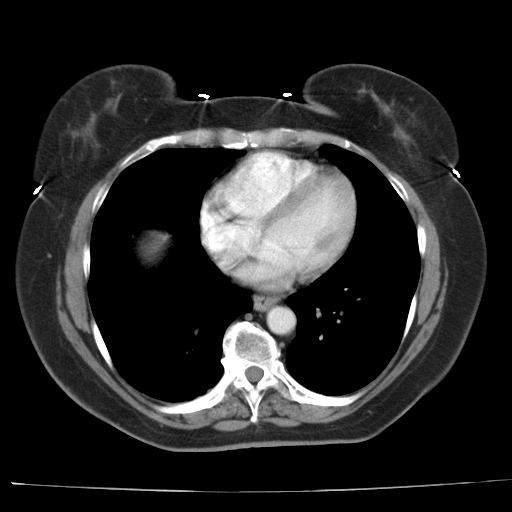
Contrast-enhanced abdominal CT, one axial slice; slice 38 of 44 in the series (ordered by position); reconstruction kernel AA-1; 140 kVp; intravenous contrast given; soft-tissue window (W 400 / L 40 HU); 5 mm slice thickness; 512 × 512 image matrix, field of view 373 × 373 mm. Female patient. Case-level facts recorded for this patient, not image findings: diagnosis: colorectal cancer liver metastases, imaged before liver resection; multiple liver metastases: yes; largest metastasis: 1.8 cm.
Outlined on this slice (outlined manually by an expert reader):
- liver: bounding box (x1, y1, x2, y2) in pixels: (137, 229, 169, 266)